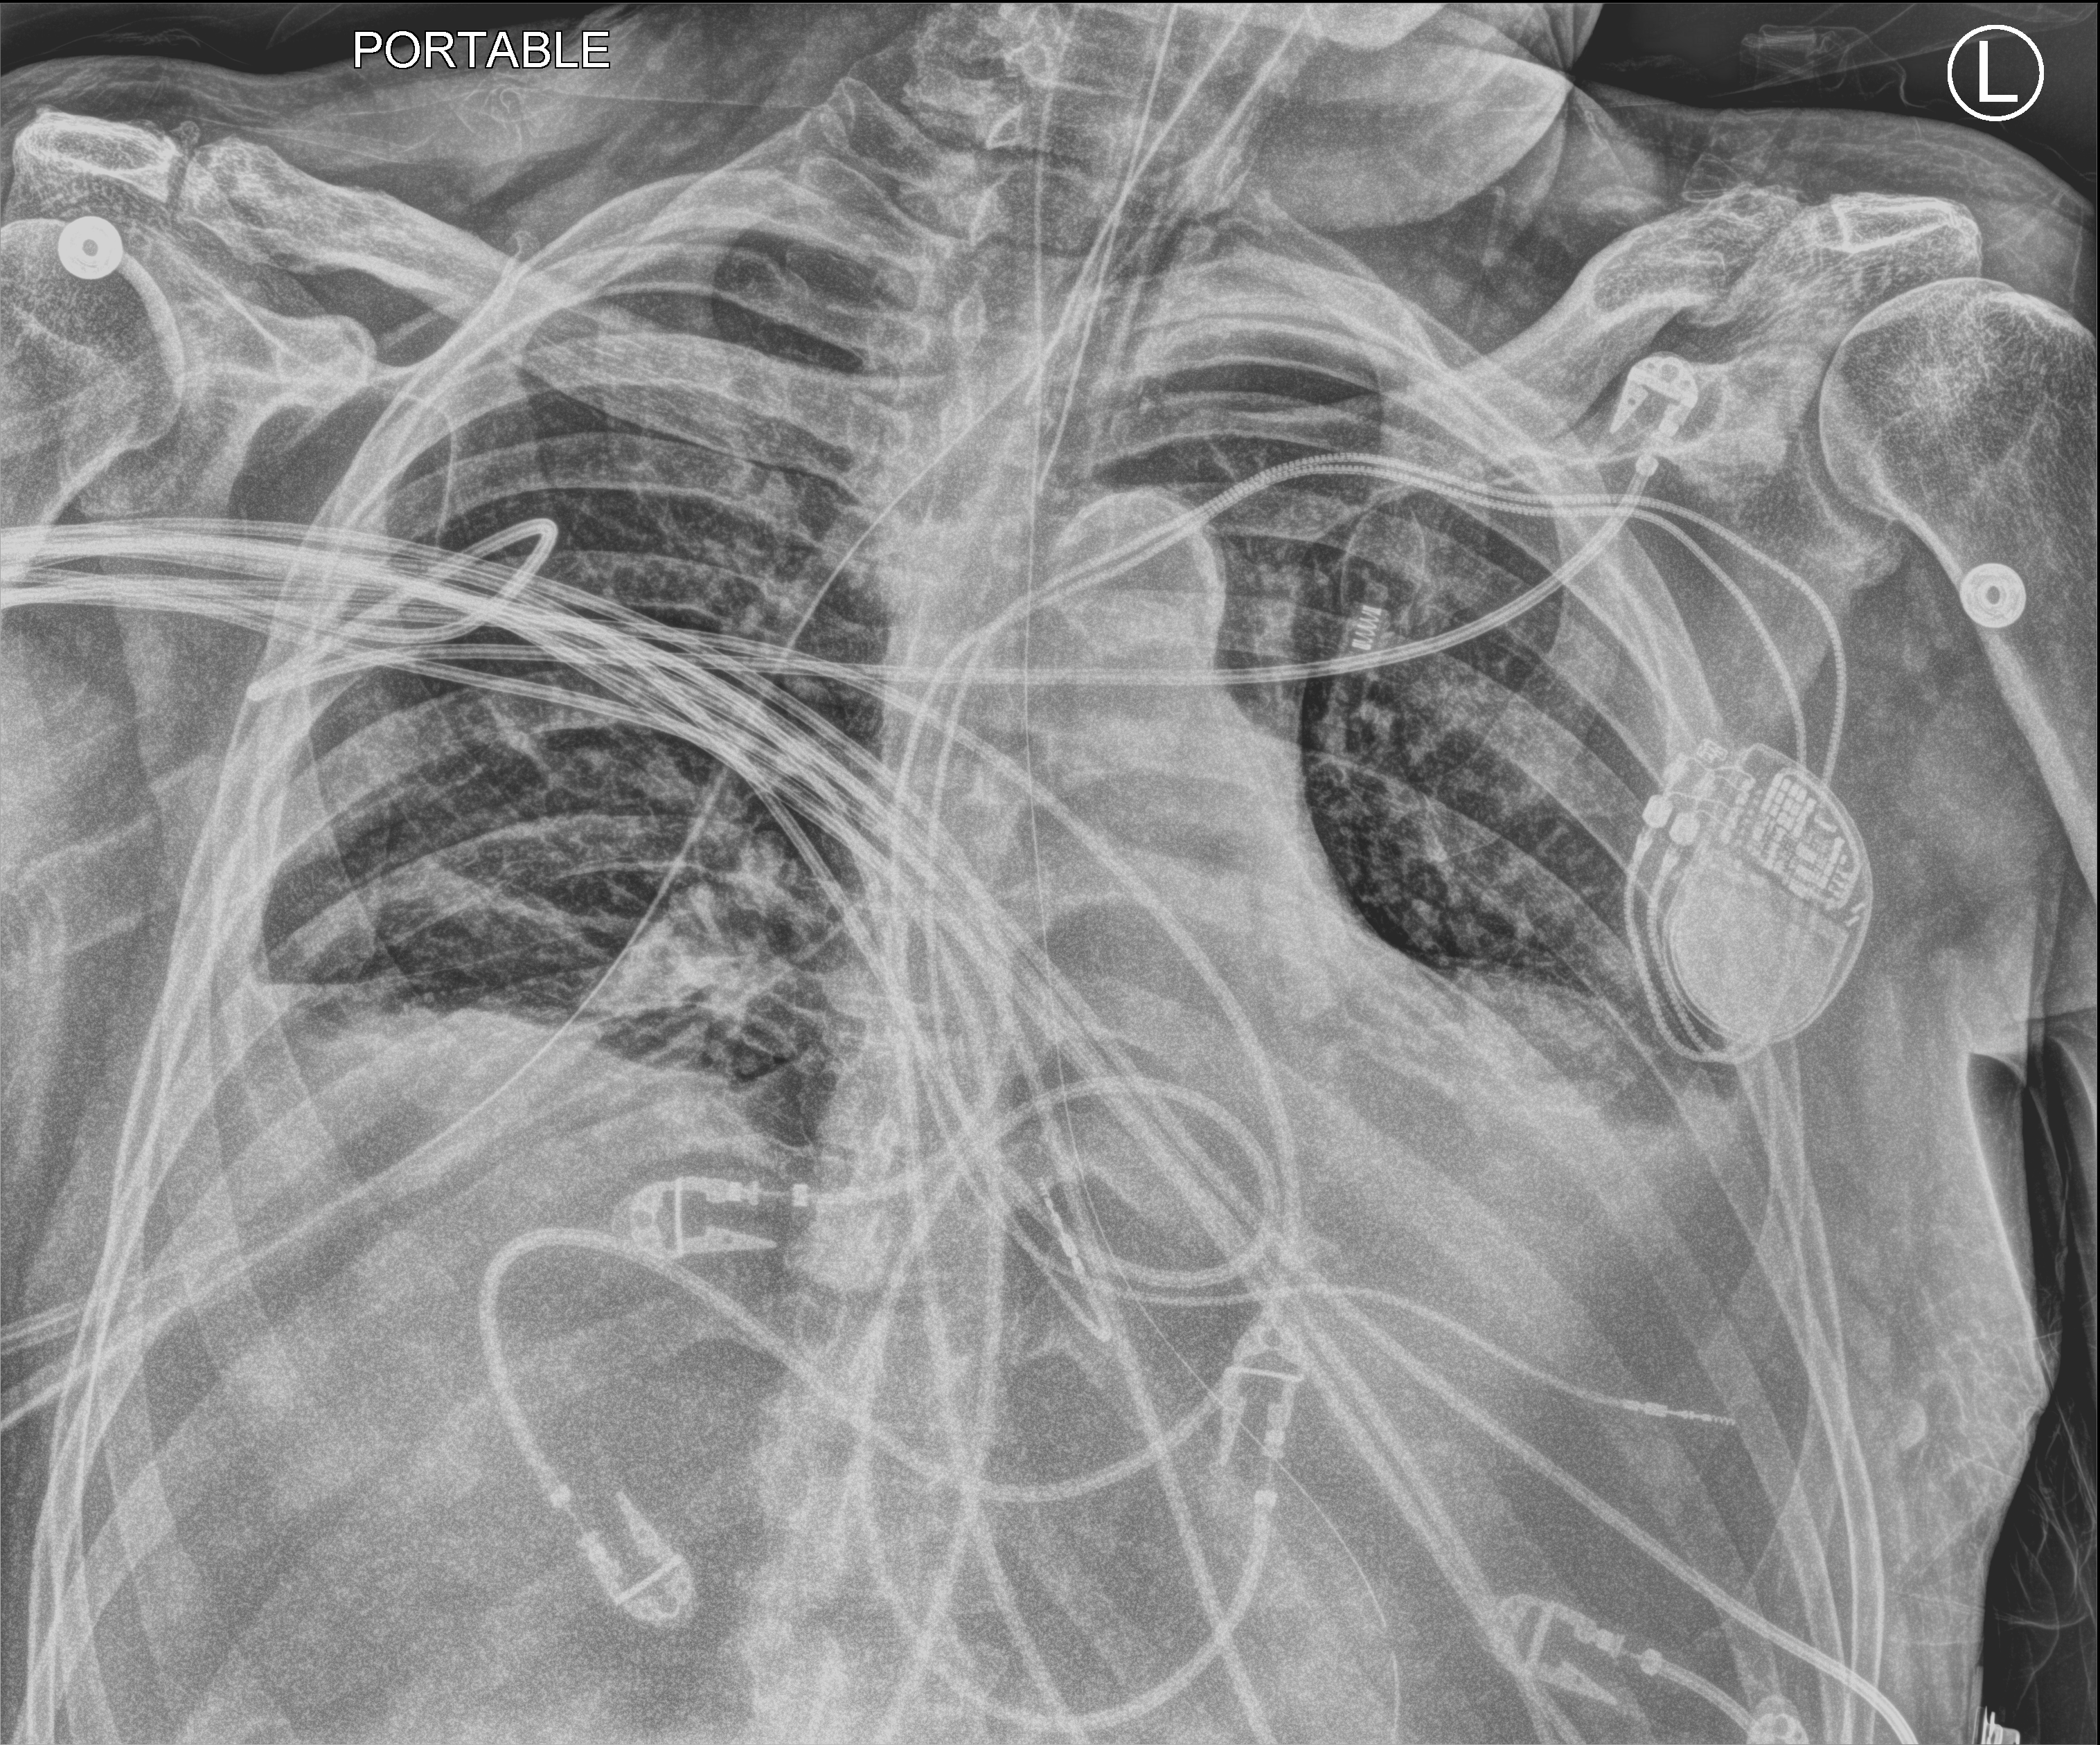
Bedside chest radiograph (computed radiography); anteroposterior (AP) projection. Male patient hospitalised with COVID-19, age 60–74 years.
Admission-level facts for this patient (not findings on this image; timing relative to this image not recorded): admitted to intensive care during this hospital stay: yes; mechanically ventilated during this hospital stay: yes; length of hospital stay: 41 days.